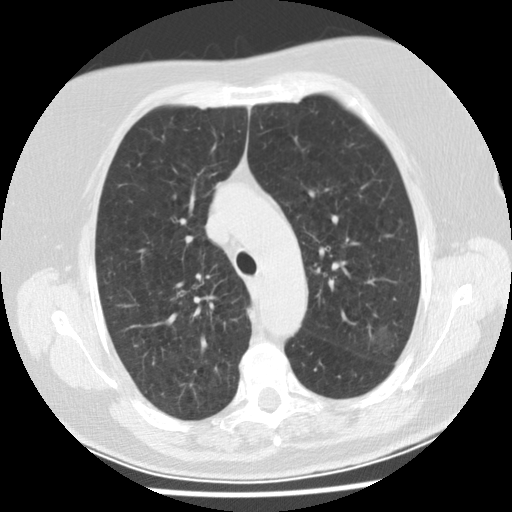
Chest CT (low-dose screening protocol), one axial image, baseline annual screen, lung window (W 1500 / L -600 HU), 2.5 mm slice thickness, 512 × 512 image matrix. Female, age 74 years at enrolment. Former smoker at enrolment.
Expert reader's lesion annotation, bounding box <335,311,408,368> (left, top, right, bottom; pixels). The screening reader recorded 2 non-calcified nodules or masses ≥4 mm on this exam (left upper lobe, left lower lobe); which of them this box marks is not recorded. Later outcome: lung cancer diagnosed 532 days after this screen — bronchiolo-alveolar adenocarcinoma, NOS, left upper lobe, stage IA (AJCC 6th edition), 20 mm at pathology.